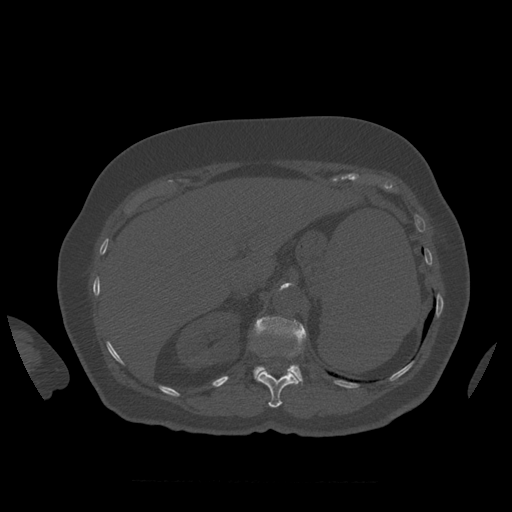
CT including the spine, one axial slice. Reconstruction kernel STANDARD. Bone window (W 1800 / L 400 HU). 1.25 mm slice thickness. 512 × 512 image matrix, field of view 404 × 404 mm. Patient age 81 years. Case-level facts recorded for this patient, not image findings: primary cancer: renal; vertebrae with lytic lesions (as recorded): L1.
Outlined on this slice (semi-automatic segmentation, software-assisted and operator-edited):
- L1 vertebra: bounding box (x1, y1, x2, y2) in pixels: (254, 317, 307, 385)
- T12 vertebra: (257, 371, 299, 408)